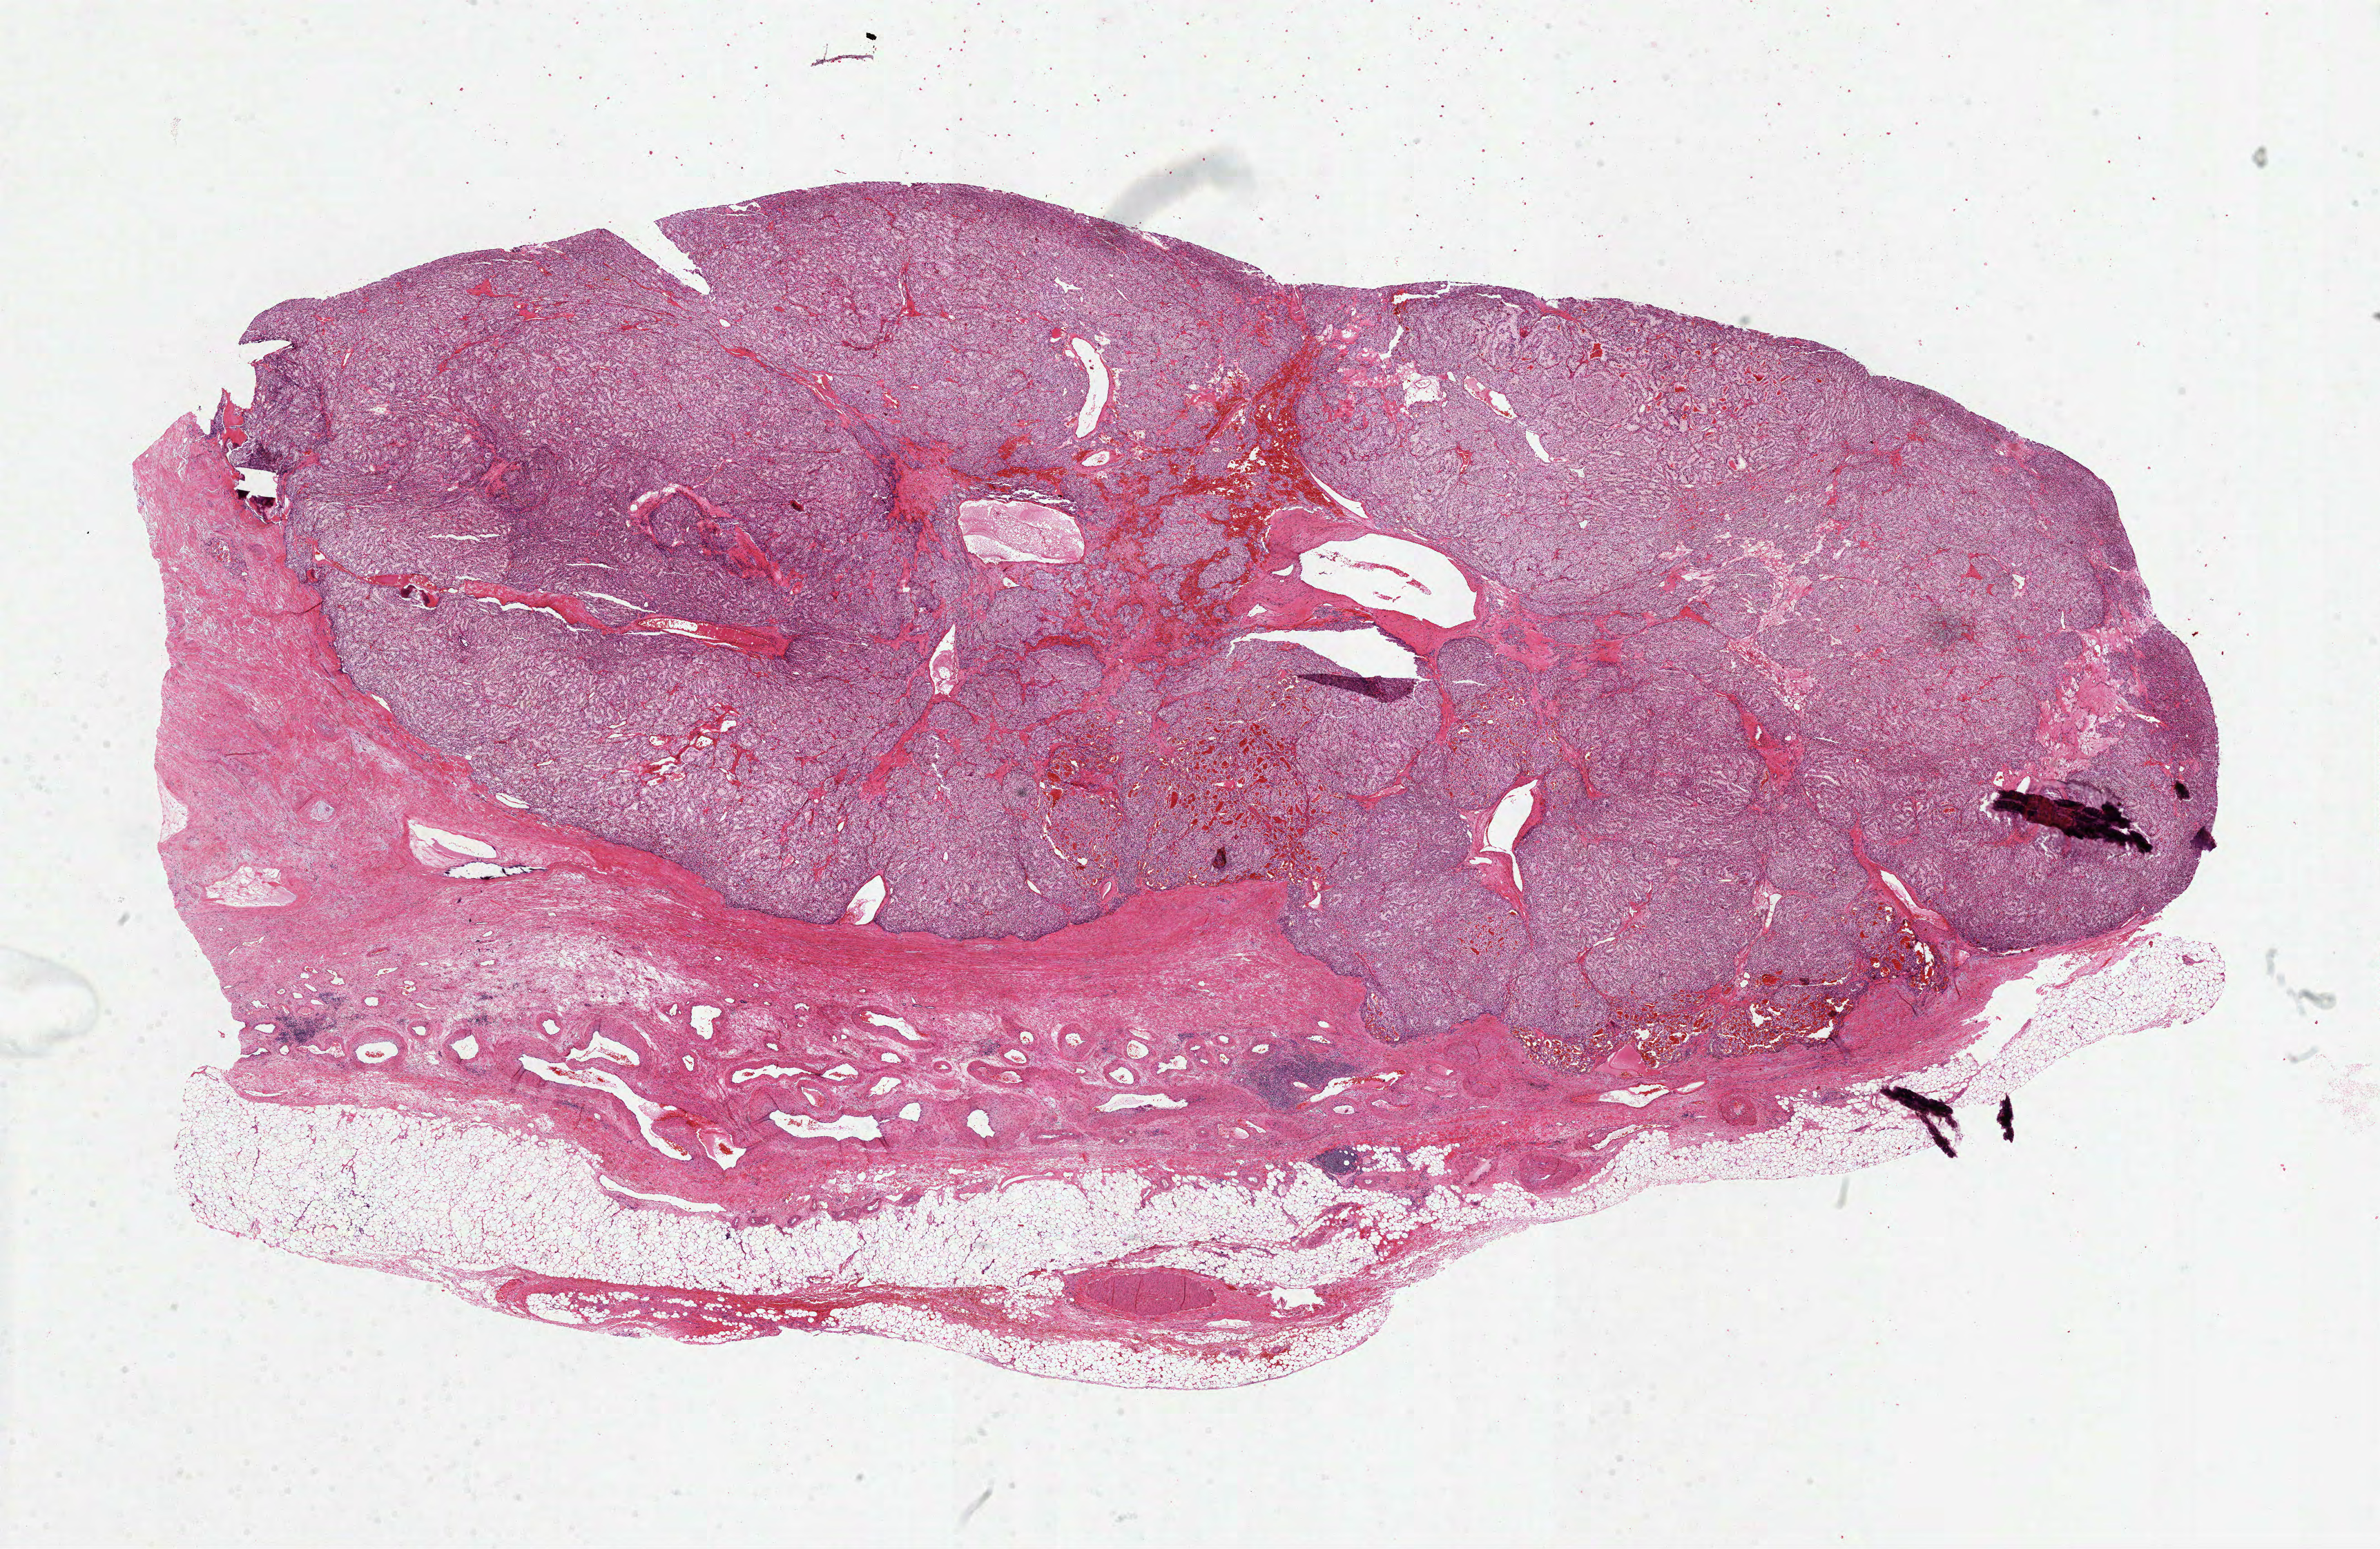
Digitized H&E-stained tissue section (whole slide) — low-resolution overview of the scanned area, about 27.8 x 18.1 mm (slide scanned at 40x), formalin-fixed paraffin-embedded (FFPE) diagnostic section, primary tumour sample from the kidney. Patient: male, age at initial diagnosis 72 years.
Histologic diagnosis: Clear cell adenocarcinoma, NOS.